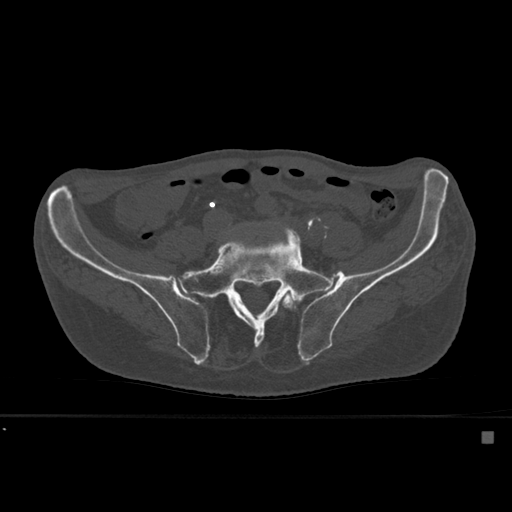
CT including the spine, one axial slice; position 162 of 527 along the scan axis; bone window (W 1800 / L 400 HU); 512 × 512 image matrix, field of view 373 × 373 mm. Male patient, age 78 years. From the clinical record (not read from this slice): primary cancer: prostate.
Outlined on this slice (semi-automatically segmented with operator editing):
- L5 vertebra: bounding box (x1, y1, x2, y2) in pixels: (282, 289, 297, 311)